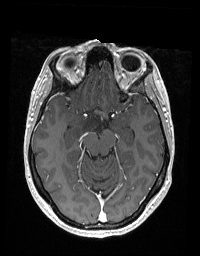
Brain MRI from a brain-tumour surgery series, one axial slice. Position 116 of 192 along the scan axis. T1-weighted post-contrast. 1 mm slice thickness. 200 × 256 image matrix, field of view 195 × 250 mm. From the clinical record (not read from this slice): histopathology: Glioblastoma; WHO grade: 2; IDH mutation: no; tumour location: Right Skull Base Temporal.
Outlined on this slice (manually delineated by an expert):
- tumour: box from (x=73, y=113) to (x=101, y=138) px